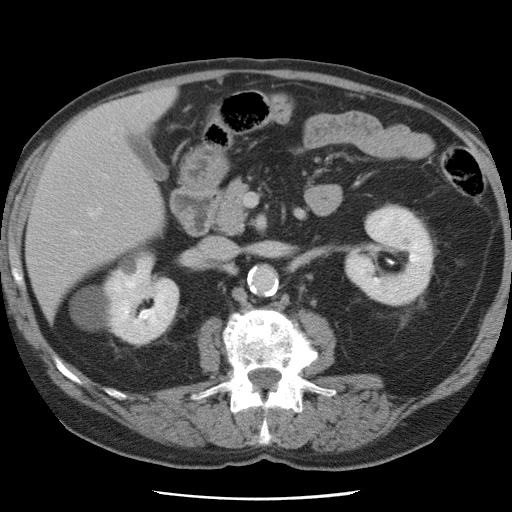
Contrast-enhanced abdominal CT, one axial slice. Position 33 of 78 along the scan axis. 120 kVp. Intravenous contrast given. Soft-tissue window (W 400 / L 40 HU). 5 mm slice thickness. 512 × 512 image matrix, field of view 337 × 337 mm. Male patient, age 75 years. From the clinical record (not read from this slice): diagnosis: colorectal cancer liver metastases, imaged before liver resection; multiple liver metastases: yes; largest metastasis: 2.4 cm; disease in both lobes: yes.
Outlined on this slice (manually delineated by an expert):
- hepatic veins: bounding box [x1, y1, x2, y2] px = [70, 207, 101, 235]
- liver: [28, 89, 174, 316]
- planned liver remnant (the part of the liver to remain after resection): [28, 117, 163, 315]
- portal vein (with intrahepatic branches): [104, 176, 107, 178]